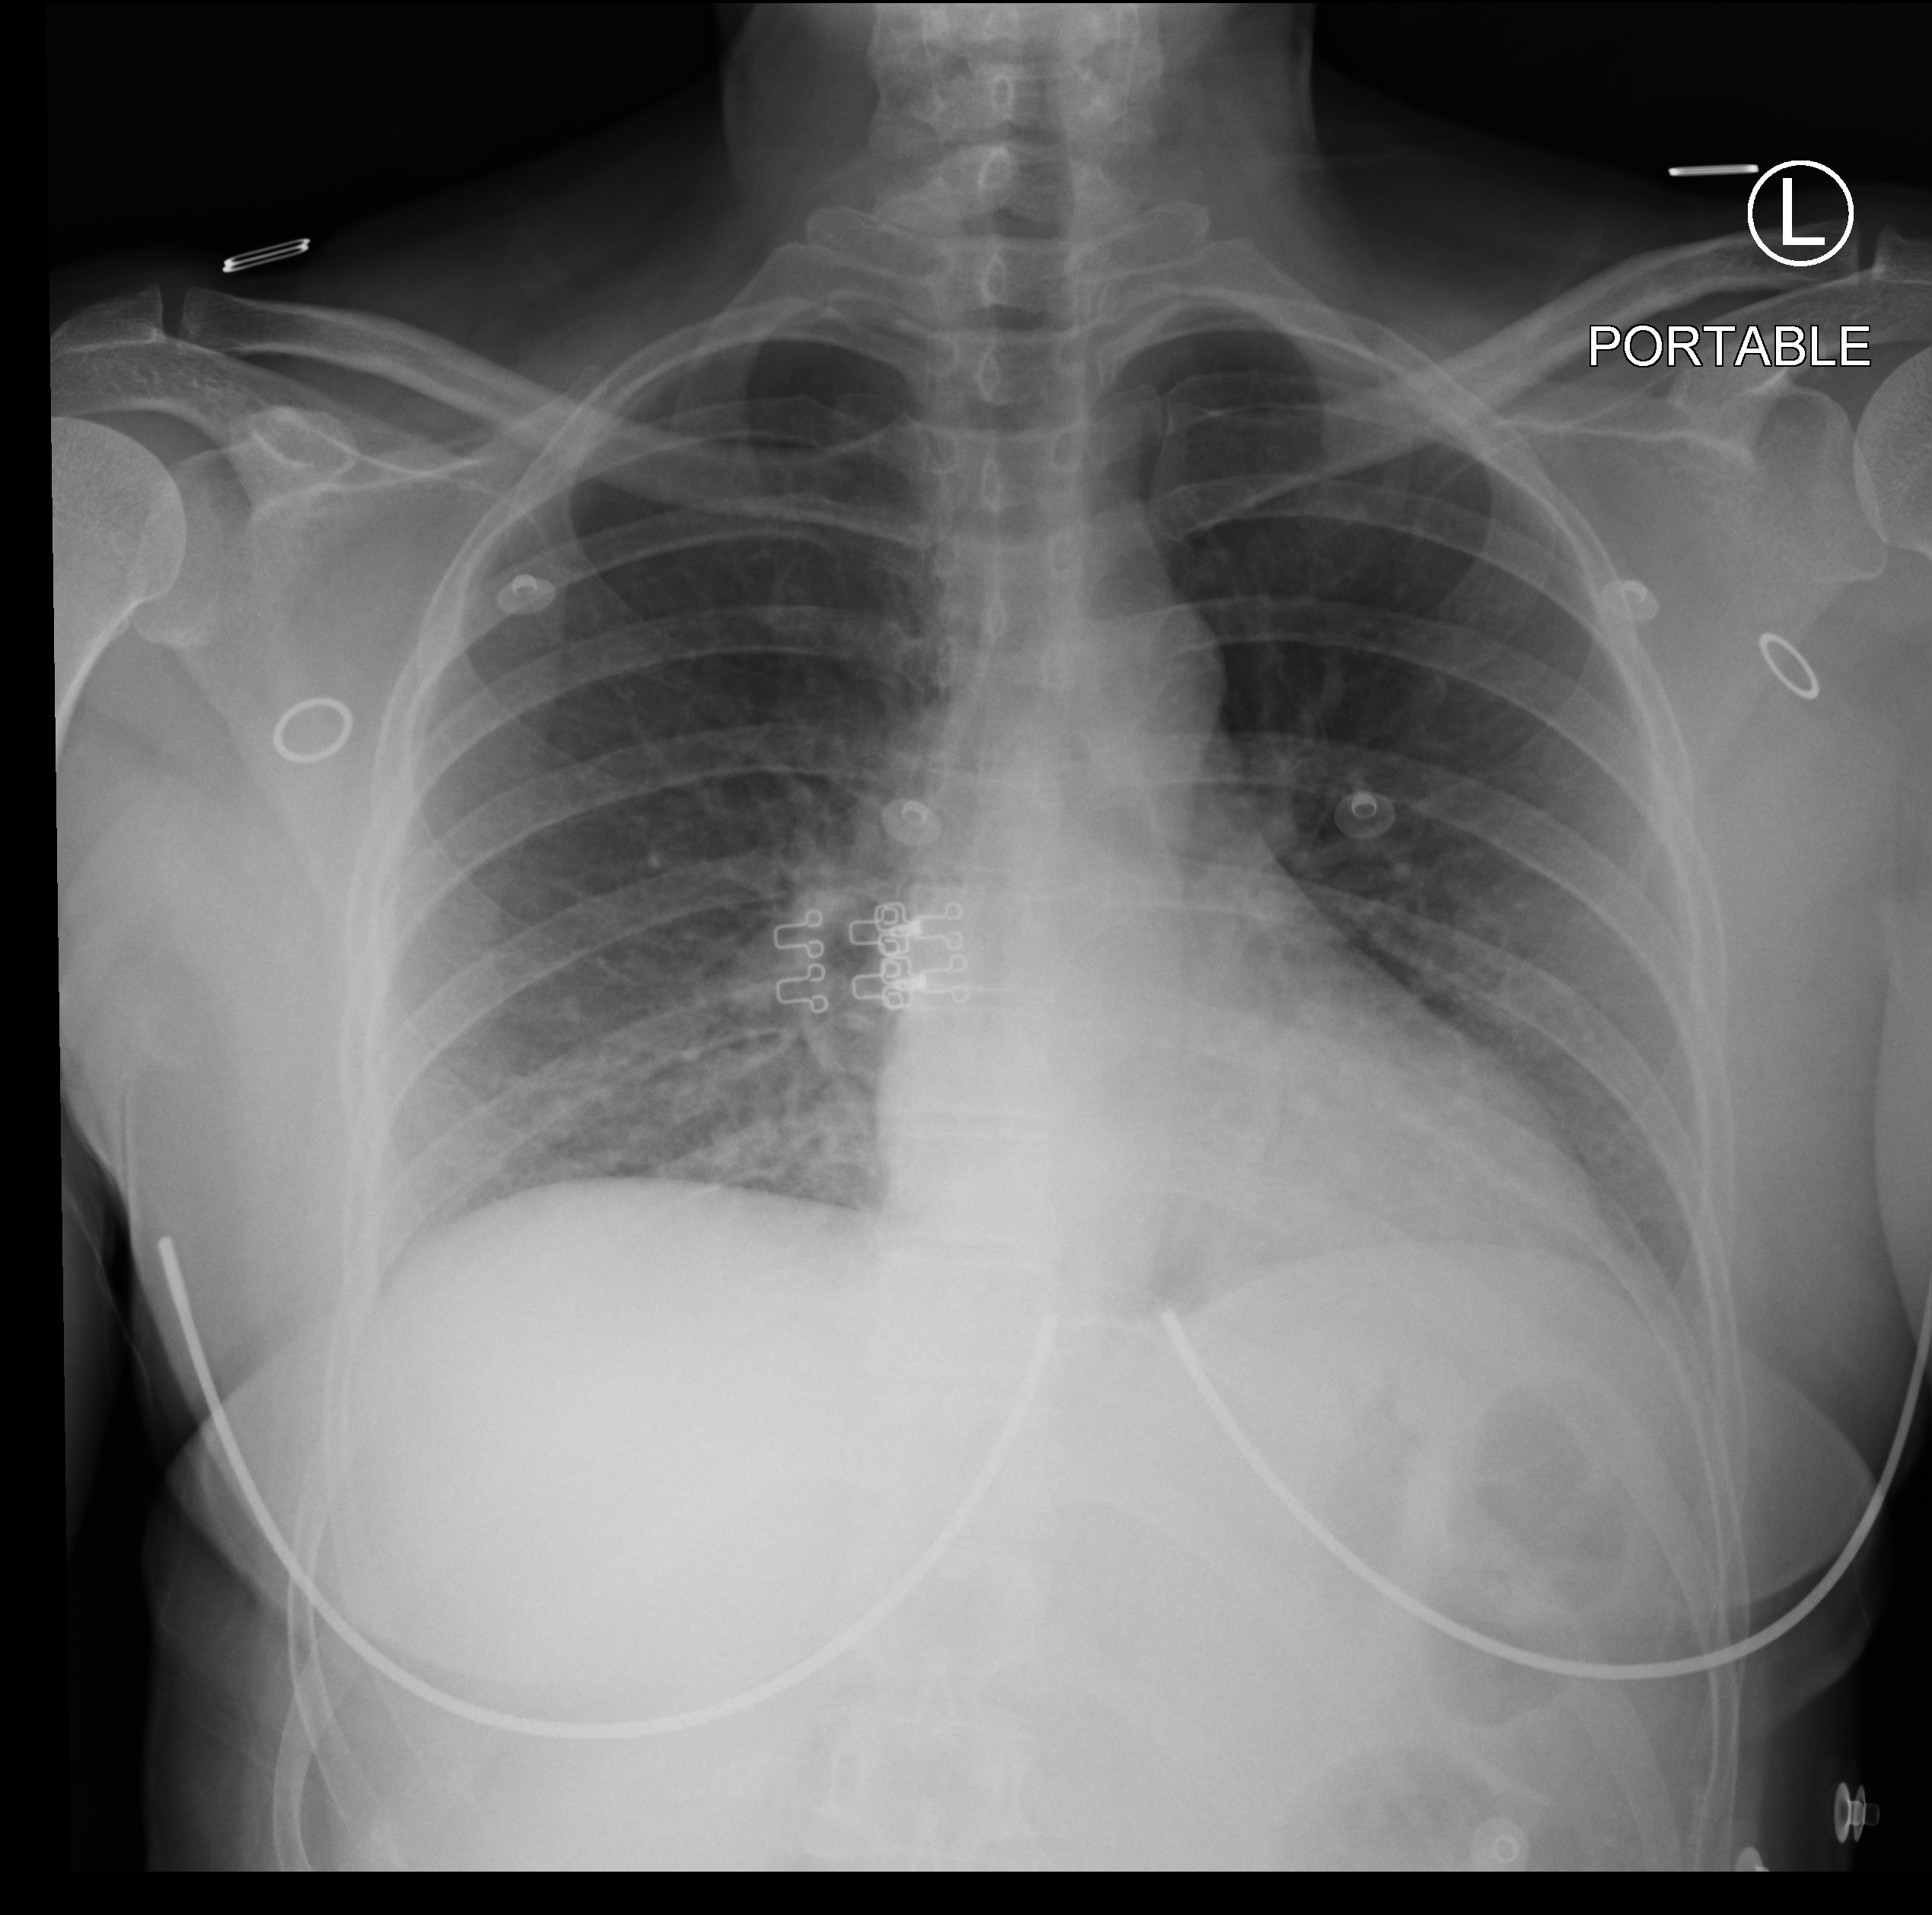
Portable chest radiograph, anteroposterior (AP) projection. Patient hospitalised with COVID-19; female, aged 18–59 years.
Hospital-stay facts (about this admission, not read from this image; timing relative to this image not recorded):
- other chronic lung disease (admission record): no
- admitted to intensive care during this hospital stay: no